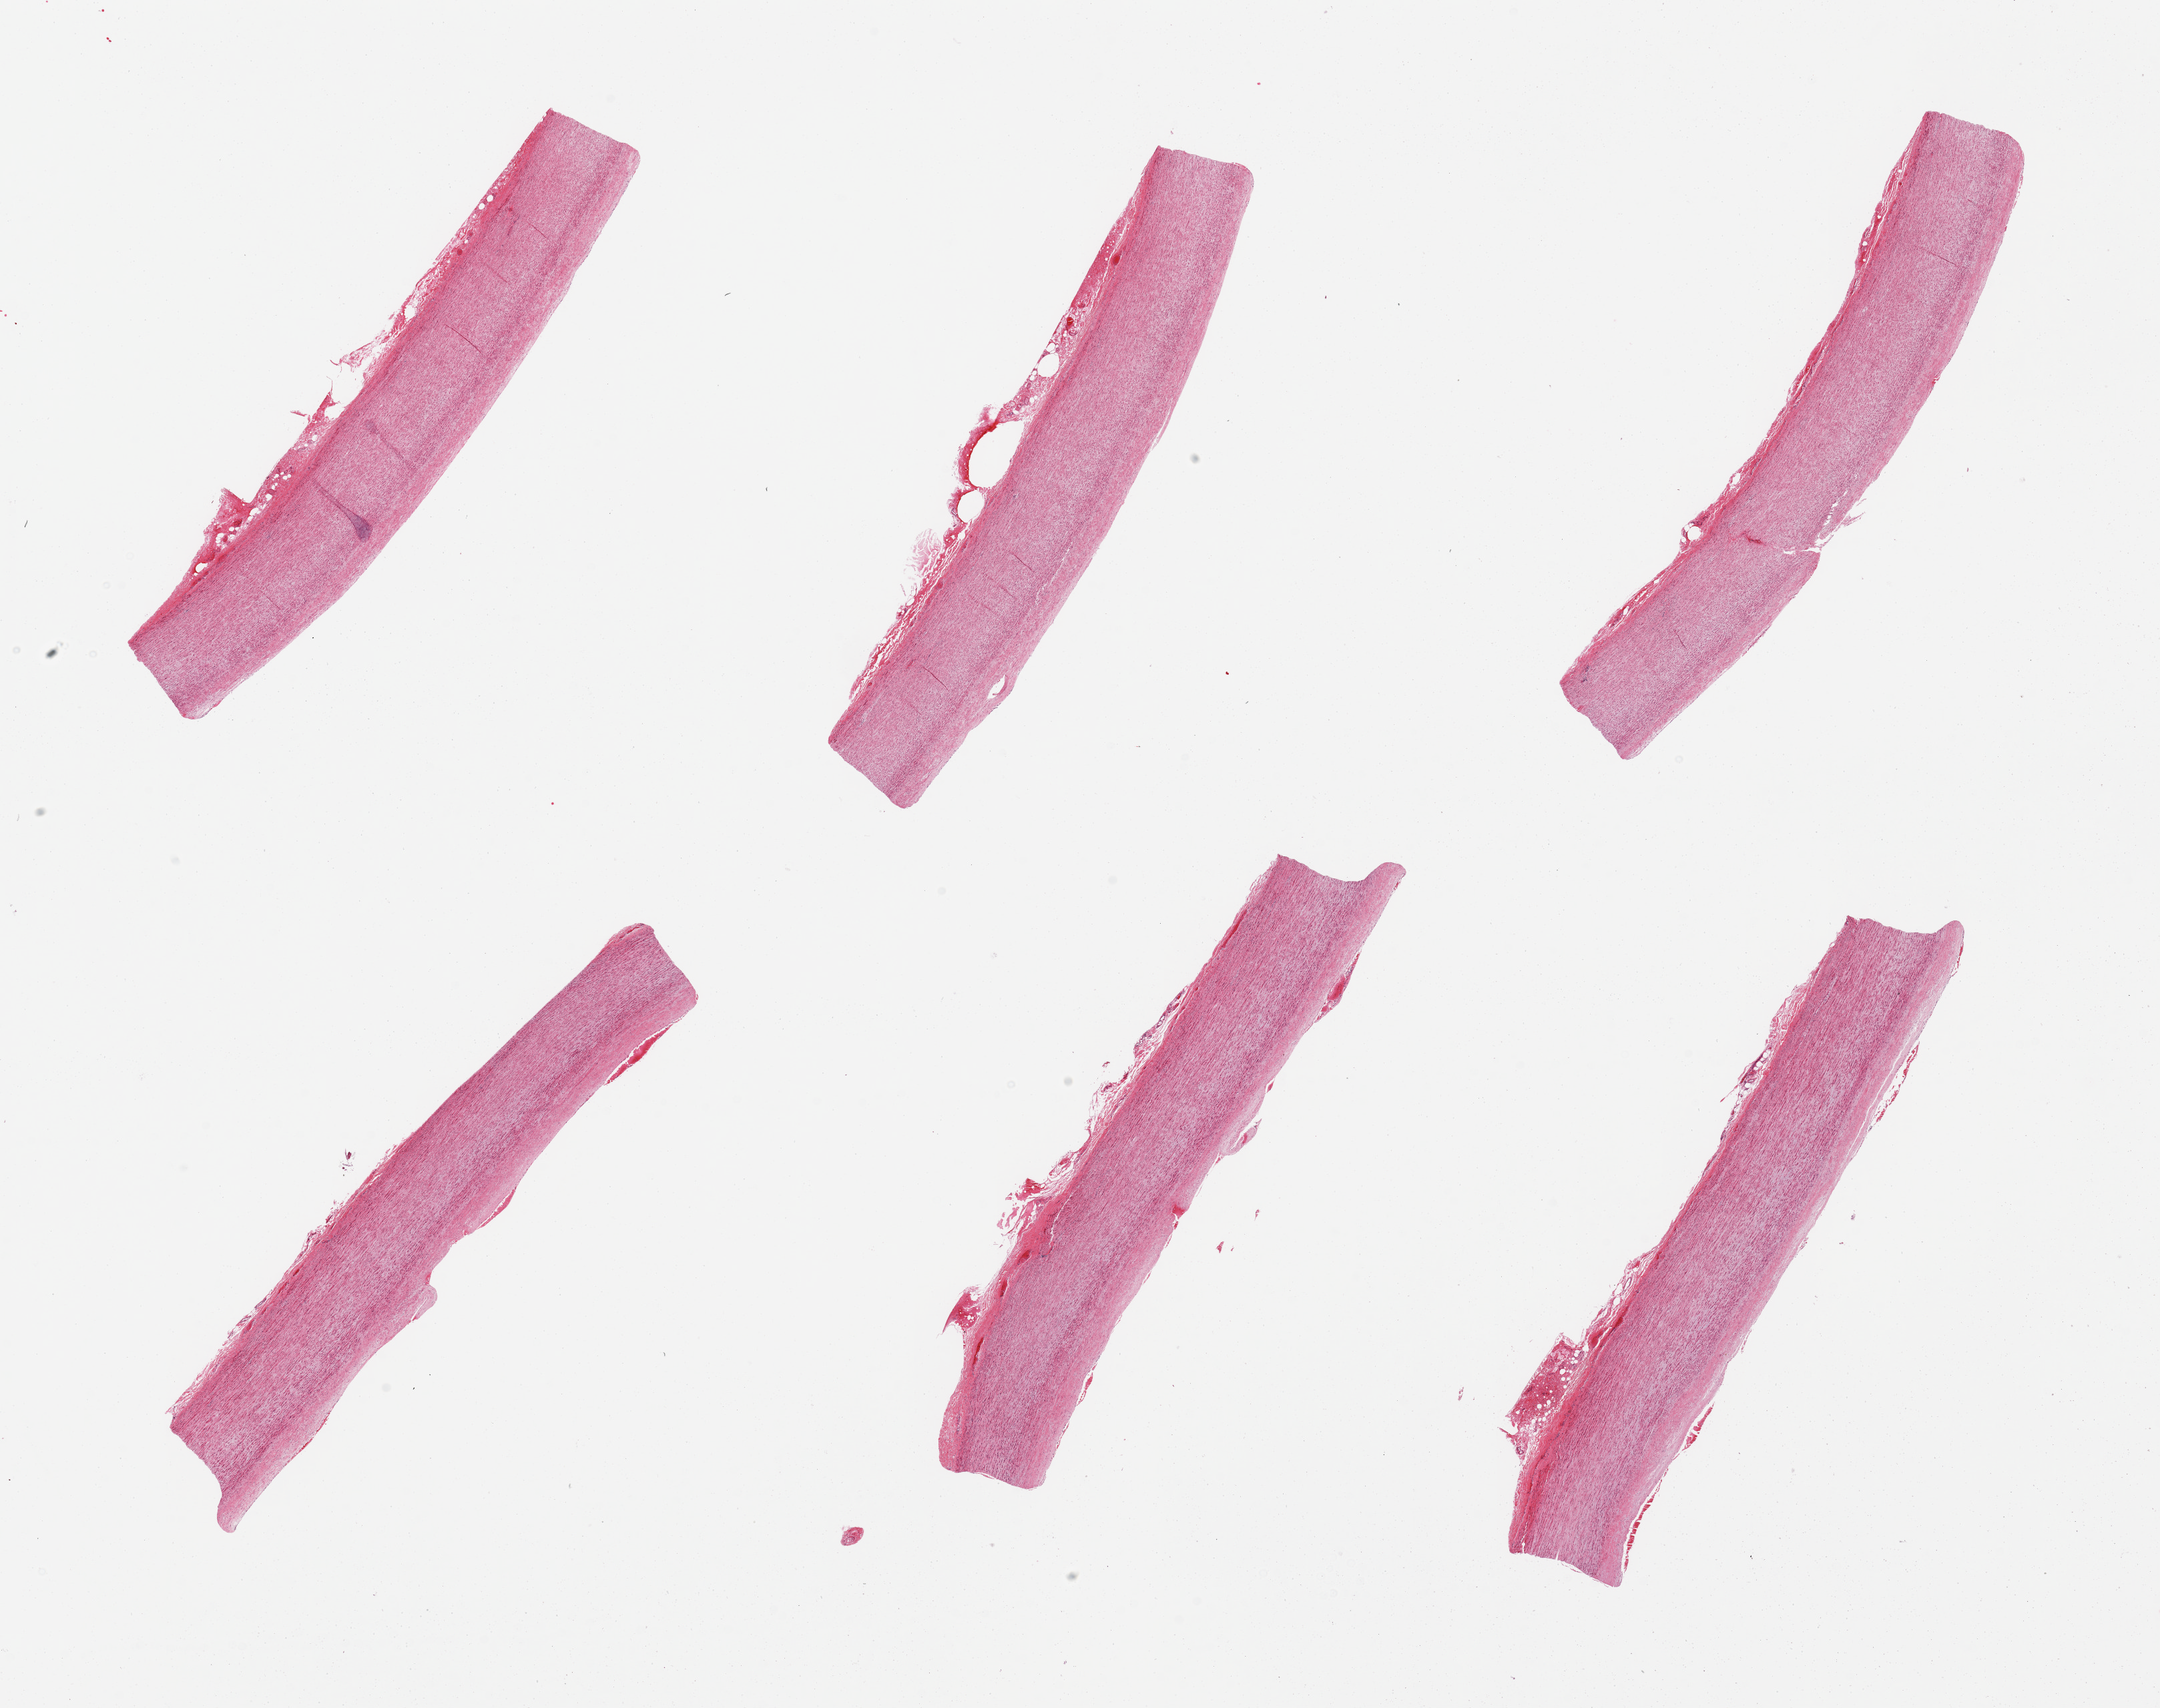
Whole-slide image, hematoxylin and eosin (H&E) stain, brightfield, a low-resolution overview of the entire scanned area, about 25.6 x 20.2 mm, PAXgene-fixed paraffin-embedded (PFPE) section, sampled site (target tissue): aorta, donor tissue sample. Donor sex: female.
Reviewer comment on this tissue sample: 6 pieces.